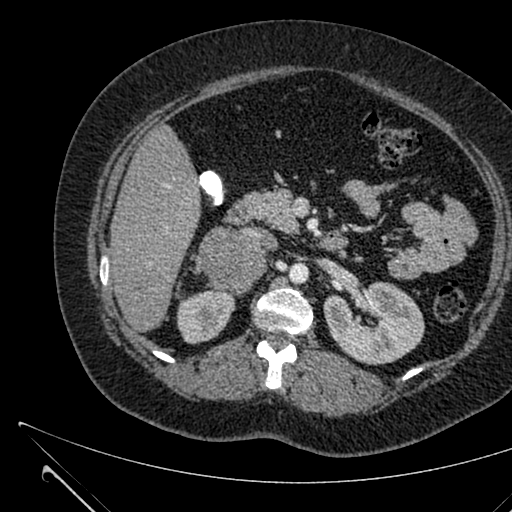
Contrast-enhanced abdominal CT, one axial slice; position 370 of 731 along the scan axis; 120 kVp; soft-tissue window (W 400 / L 40 HU); 512 × 512 image matrix, field of view 376 × 376 mm. Female patient, age 36 years. From the clinical record (not read from this slice): diagnosis: adrenocortical carcinoma; tumour side: right adrenal; tumour size at pathology: 10 cm.
Annotated regions visible in this slice (semi-automatic segmentation, software-assisted and operator-edited):
- mass: box from (x=200, y=228) to (x=265, y=294) px